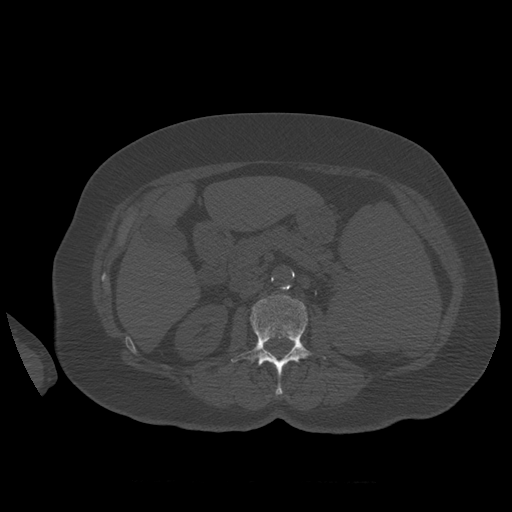
CT including the spine, one axial slice; position 254 of 399 along the scan axis; reconstruction kernel STANDARD; 120 kVp; bone window (W 1800 / L 400 HU); 512 × 512 image matrix, field of view 404 × 404 mm. Patient age 81 years. Case-level facts recorded for this patient, not image findings: primary cancer: renal.
Annotated regions visible in this slice (semi-automatically segmented with operator editing):
- L2 vertebra: box from (x=231, y=295) to (x=326, y=395) px